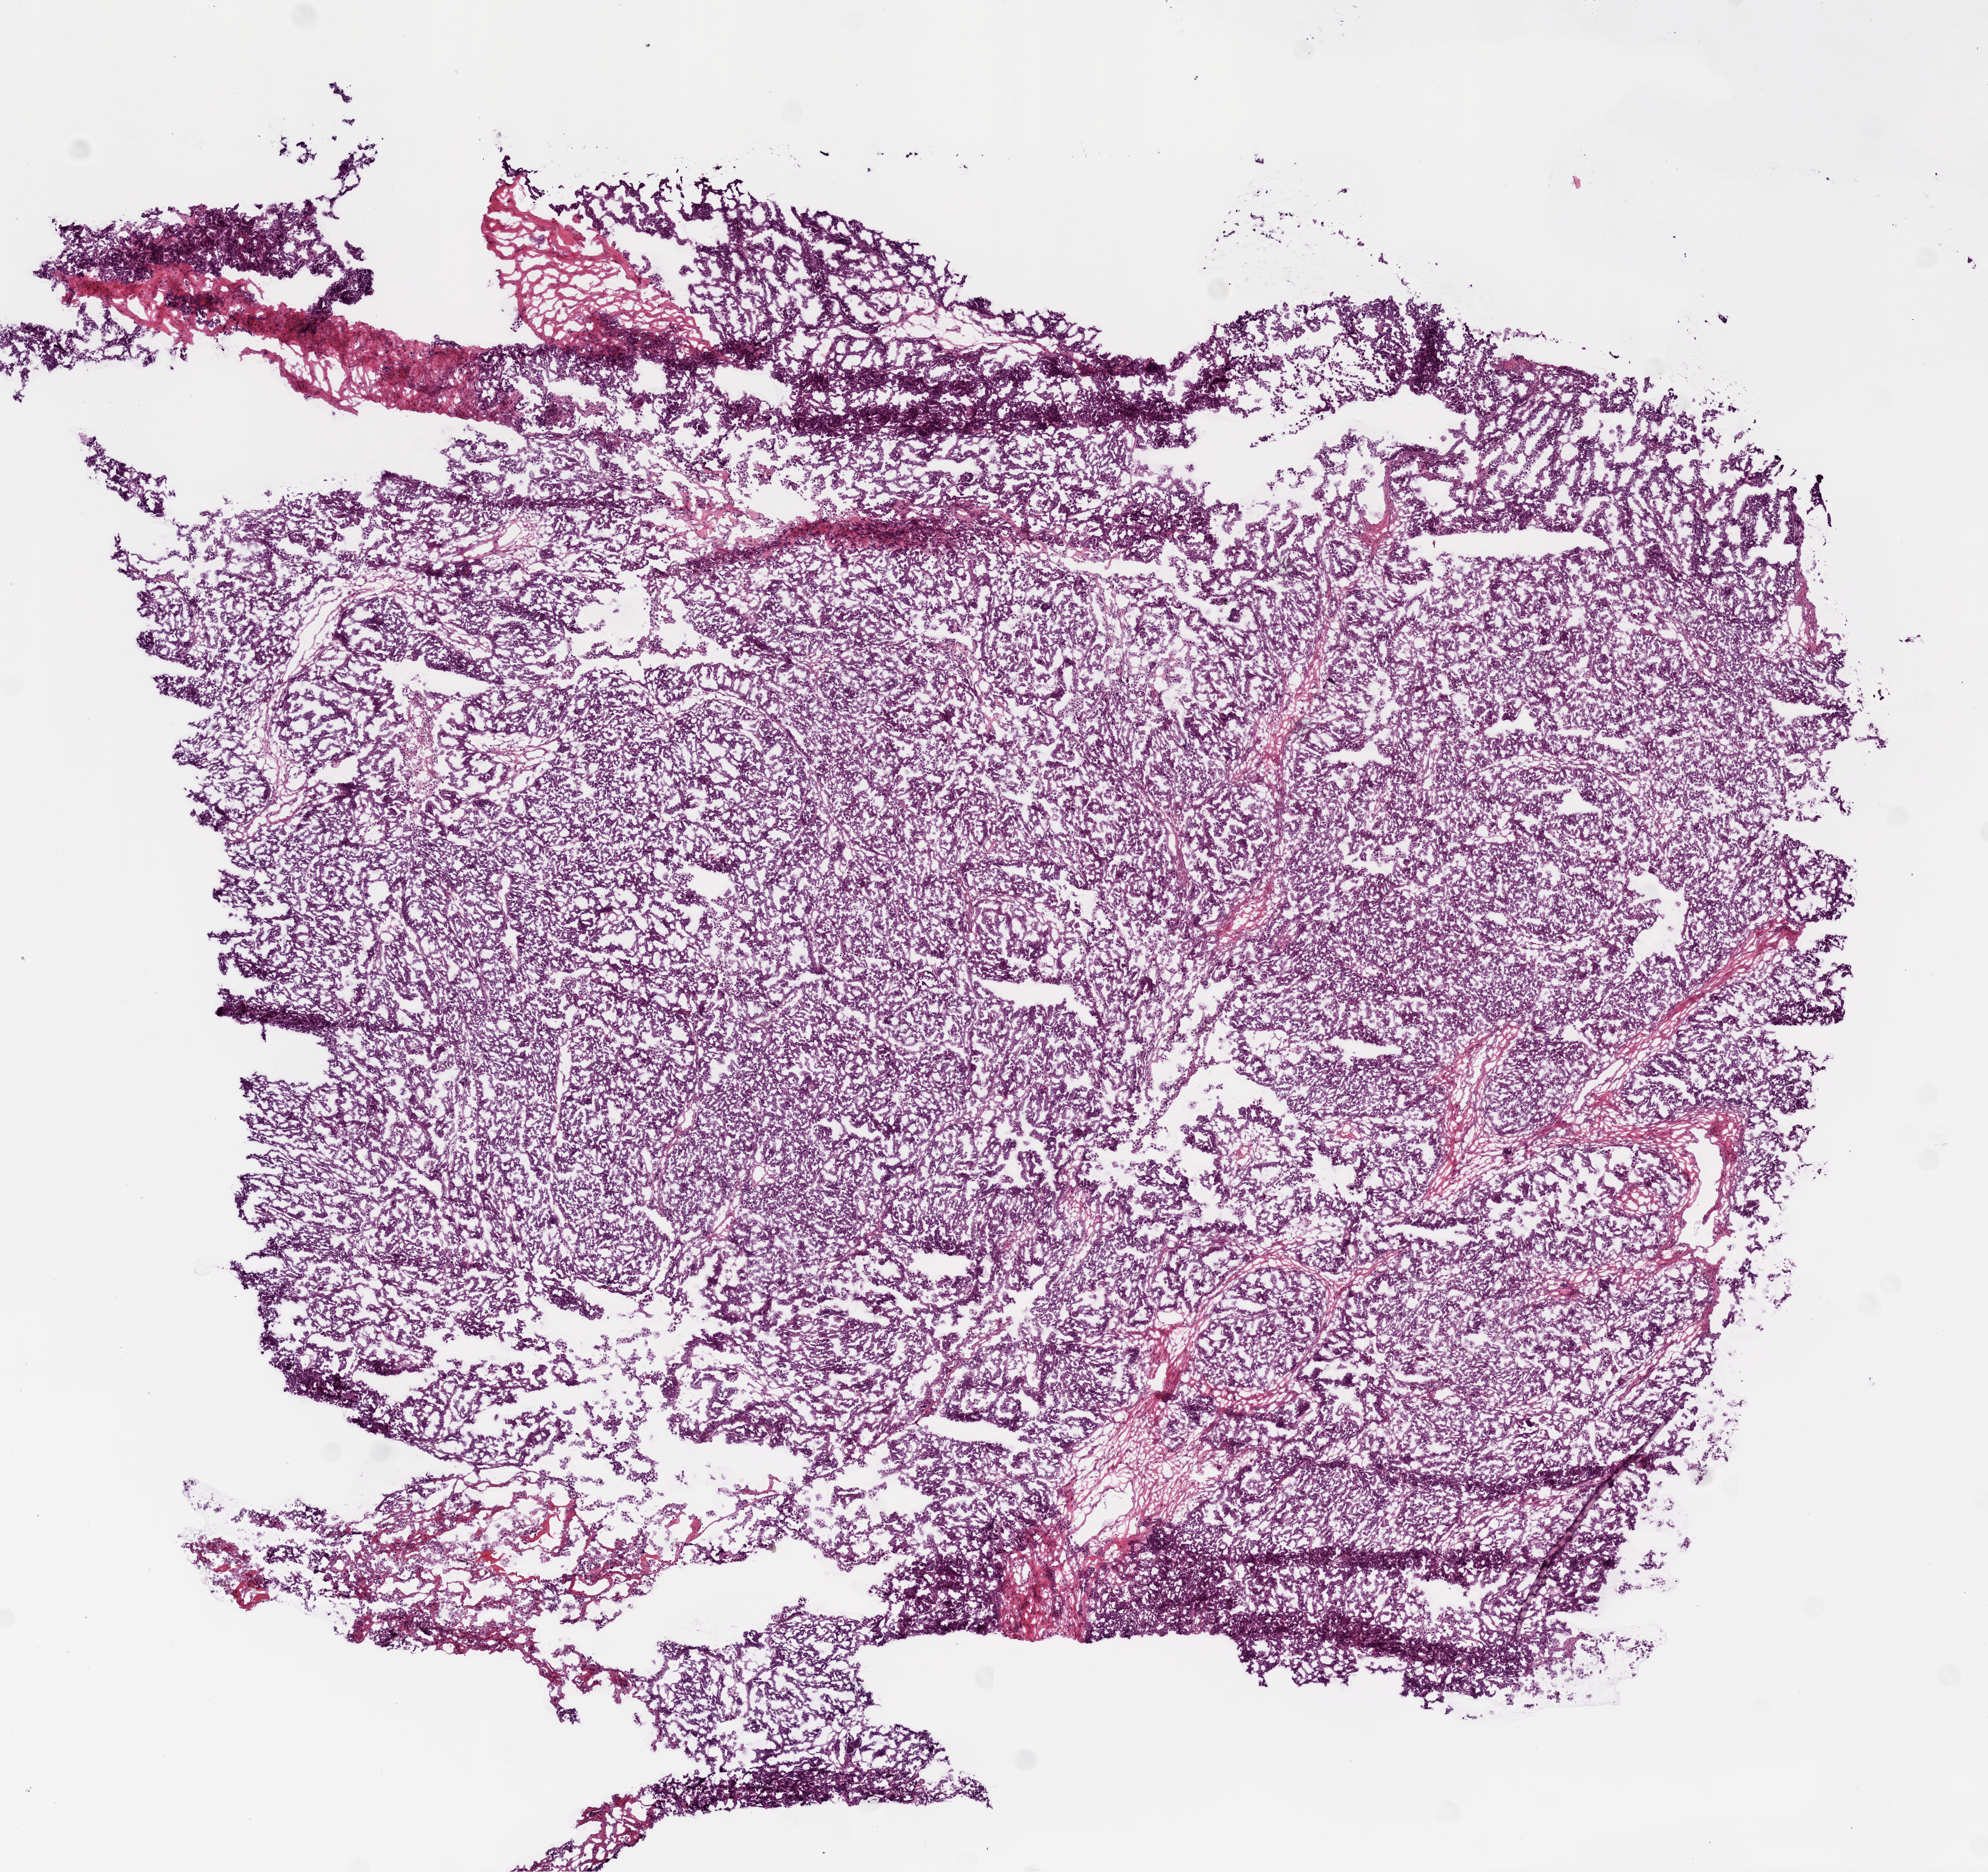
H&E-stained whole-slide image — low-resolution overview of the scanned area, about 8.0 x 7.6 mm (acquisition: 20x scan). Frozen section from the bottom of the tissue portion. Ovary, primary tumour sample. Female patient; age at initial diagnosis 48 years. Composition of this section per pathologist review: tumour cells 98%, tumour nuclei 99%.
Histologic diagnosis: Serous cystadenocarcinoma, NOS.